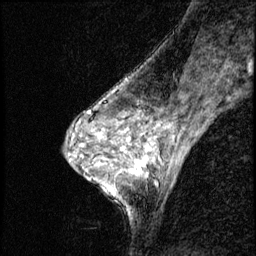
Breast MRI (dynamic contrast-enhanced), one sagittal slice; slice 33 of 56 in the series (ordered by position); dynamic contrast-enhanced series, image 2 of 3 at this slice position (ordered by acquisition); 1.5 T; TE 4.2 ms, TR 8.7 ms; 2.5 mm slice thickness; 256 × 256 image matrix. Patient: female, 50 years. Case-level facts recorded for this patient, not image findings: setting: breast cancer imaged before/during neoadjuvant chemotherapy; receptor status: HR-positive, HER2-negative.
Structures marked on this image (semi-automatic segmentation, software-assisted and operator-edited):
- analysis volume of interest (the breast-tissue region the enhancement analysis was run in; not a lesion): bounding box <119,136,169,190> (left, top, right, bottom; pixels)
- tumour enhancement mask (voxels above the 140 % enhancement threshold inside the analysis volume of interest): <122,147,154,176>